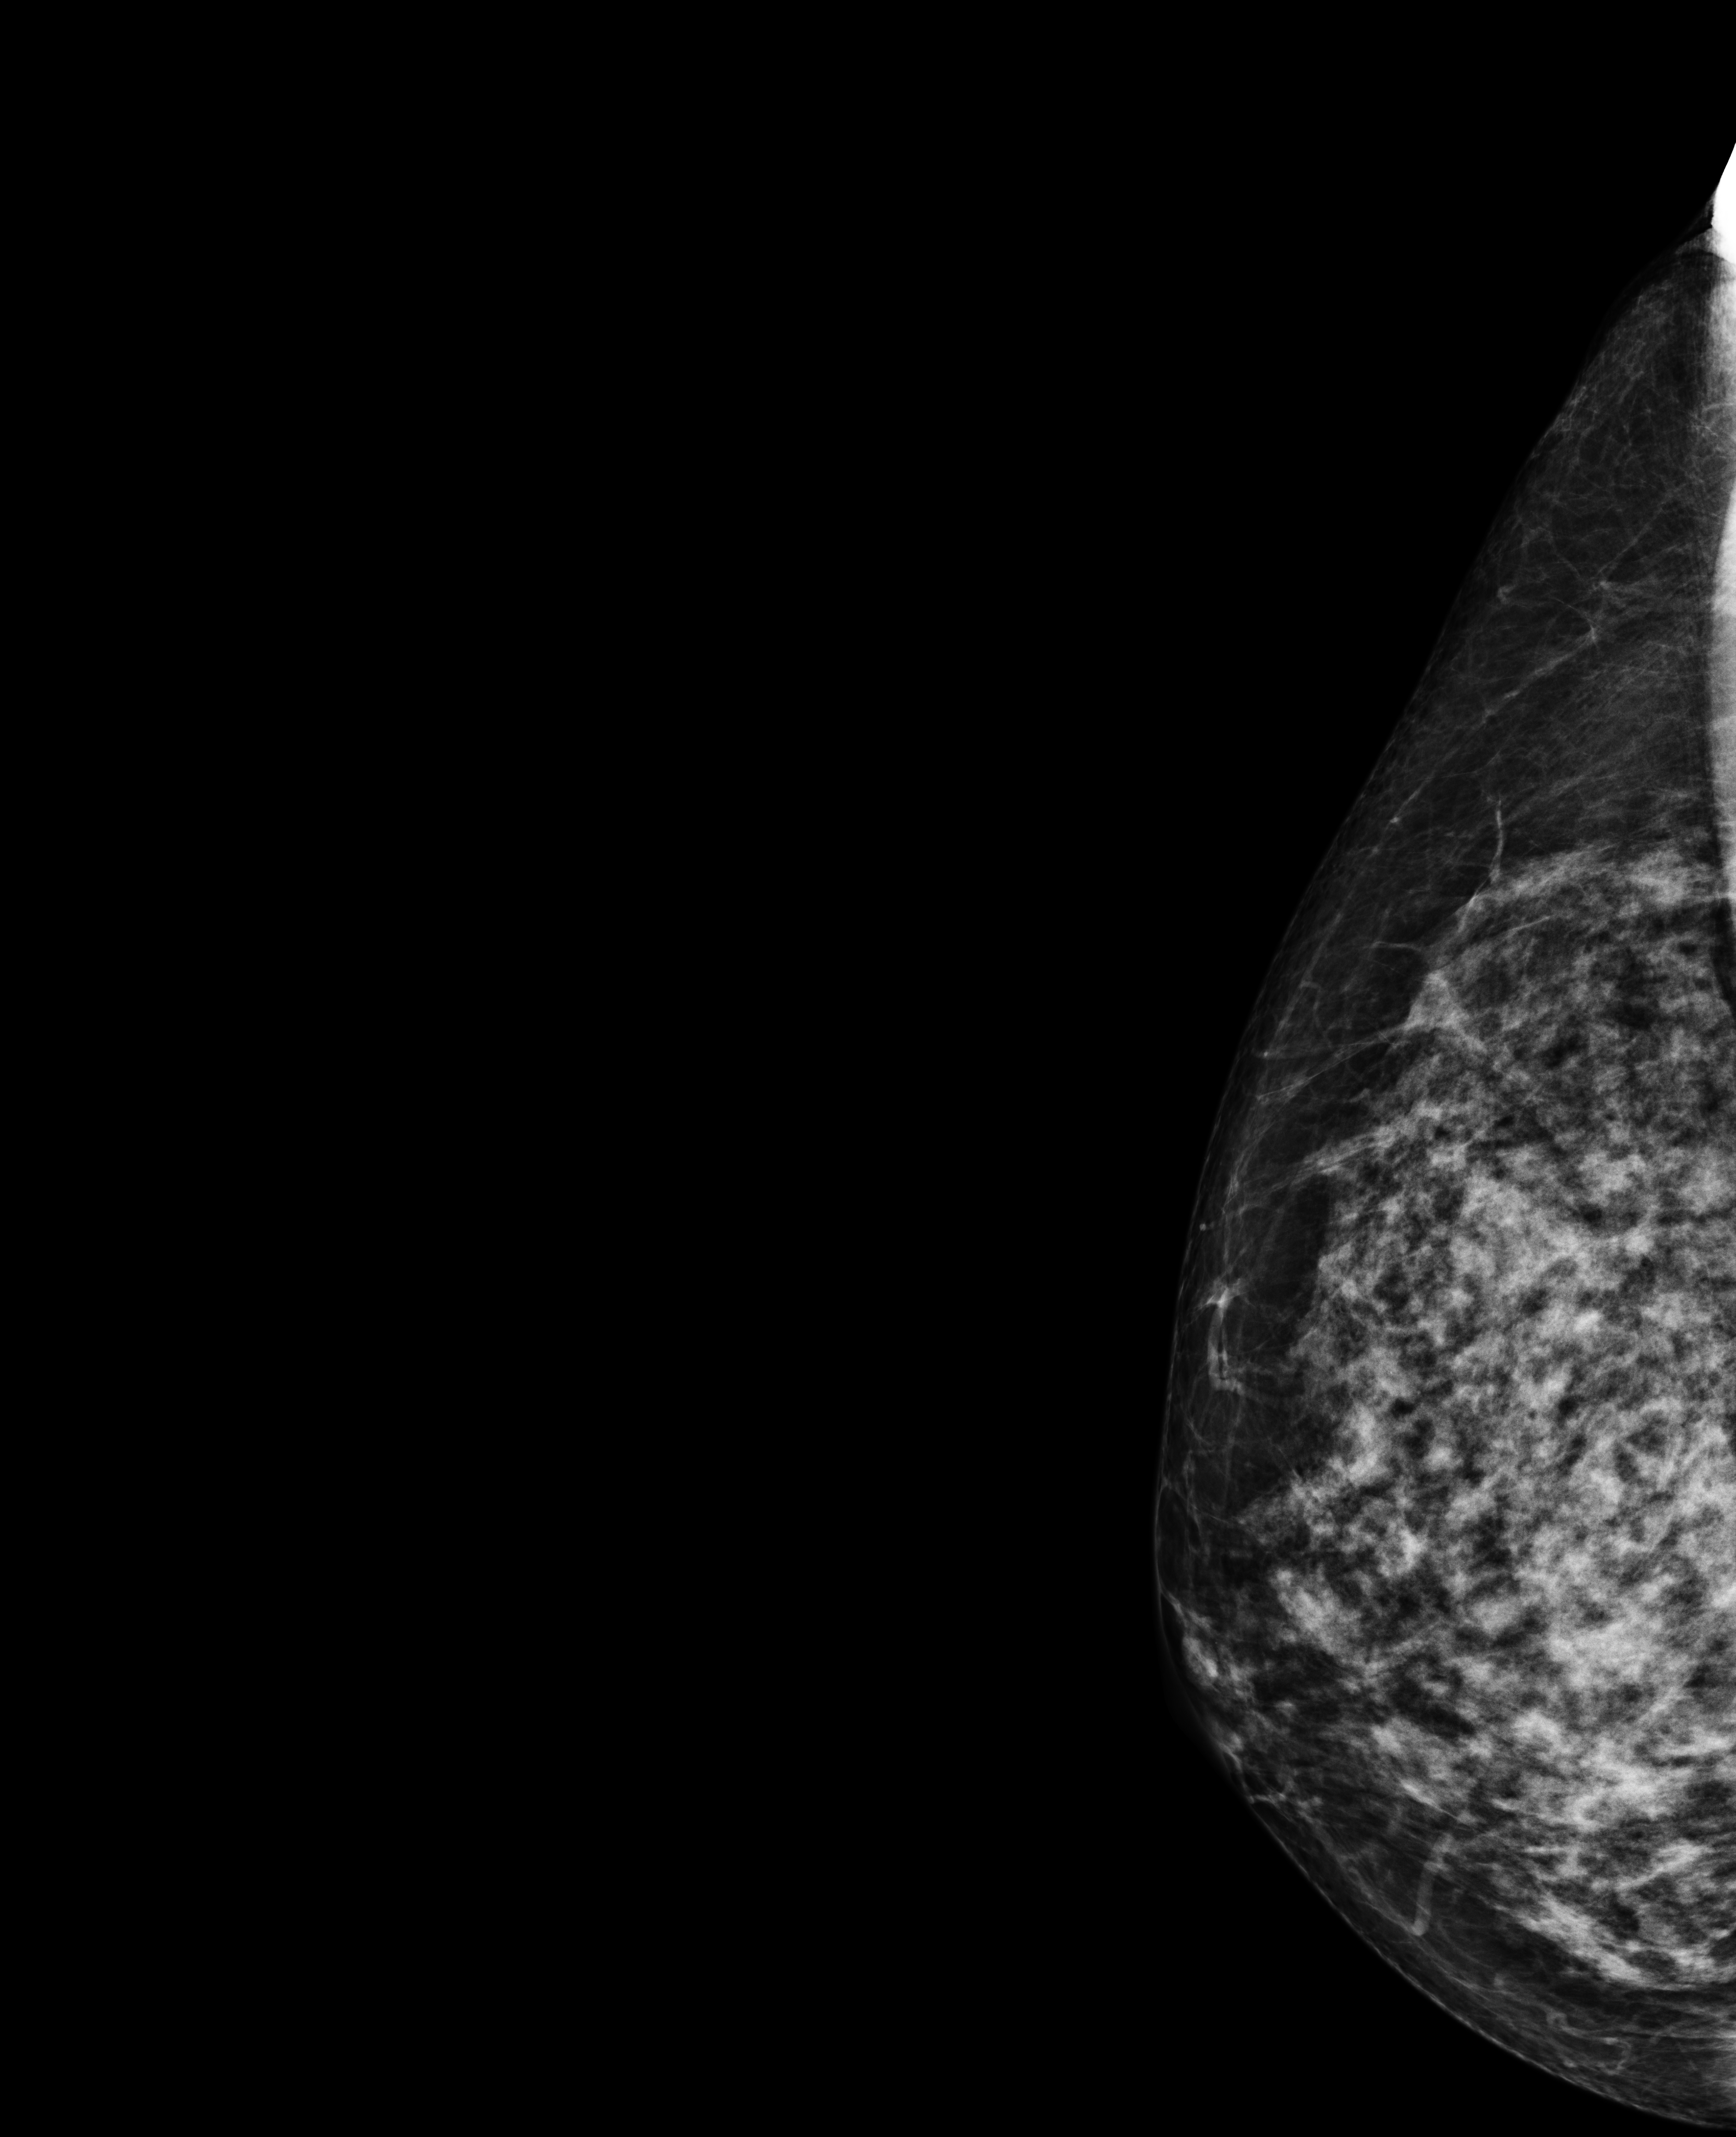
Digital mammogram (FFDM), right breast, laterally exaggerated craniocaudal (XCCL) view (axillary tissue), annual screening mammography examination, system: Selenia Dimensions. Patient aged 43 years (female).
Breast density at the screening exam (both breasts): extremely dense (BI-RADS density category d). Final BI-RADS category for the screening round (tomosynthesis exam, both breasts): category 2. Recall: recalled for additional imaging after this screen.